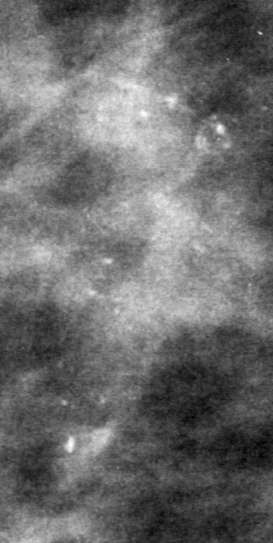
Crop from a digitized film mammogram around one marked abnormality, right breast, CC view.
Marked abnormality: calcifications, morphology pleomorphic, distribution linear; BI-RADS assessment category 4; subtlety rating 3 on a 1 (subtle) to 5 (obvious) scale; pathology (as recorded): malignant.